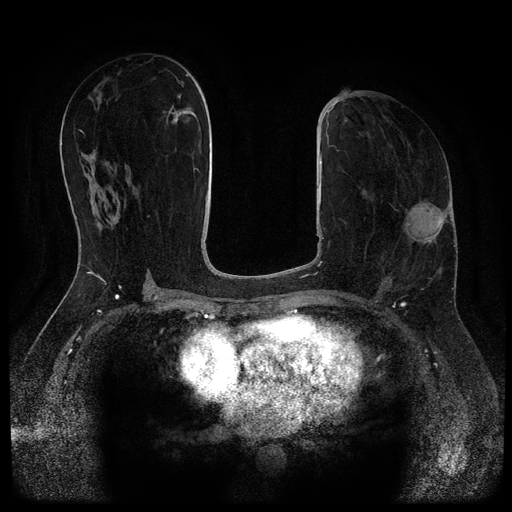
Breast MRI (dynamic contrast-enhanced, multi-phase), one axial slice; position 50 of 116 along the scan axis; dynamic contrast-enhanced series, time point 2 of 5 at this slice position (early post-contrast); 1.5 T; TE 2.7 ms, TR 5.4 ms; 512 × 512 image matrix. Patient: female, 58 years.
Annotated regions visible in this slice (semi-automatically segmented with operator editing):
- breast lesion (labelled benign in the annotation): bounding box <172,107,189,125> (left, top, right, bottom; pixels)